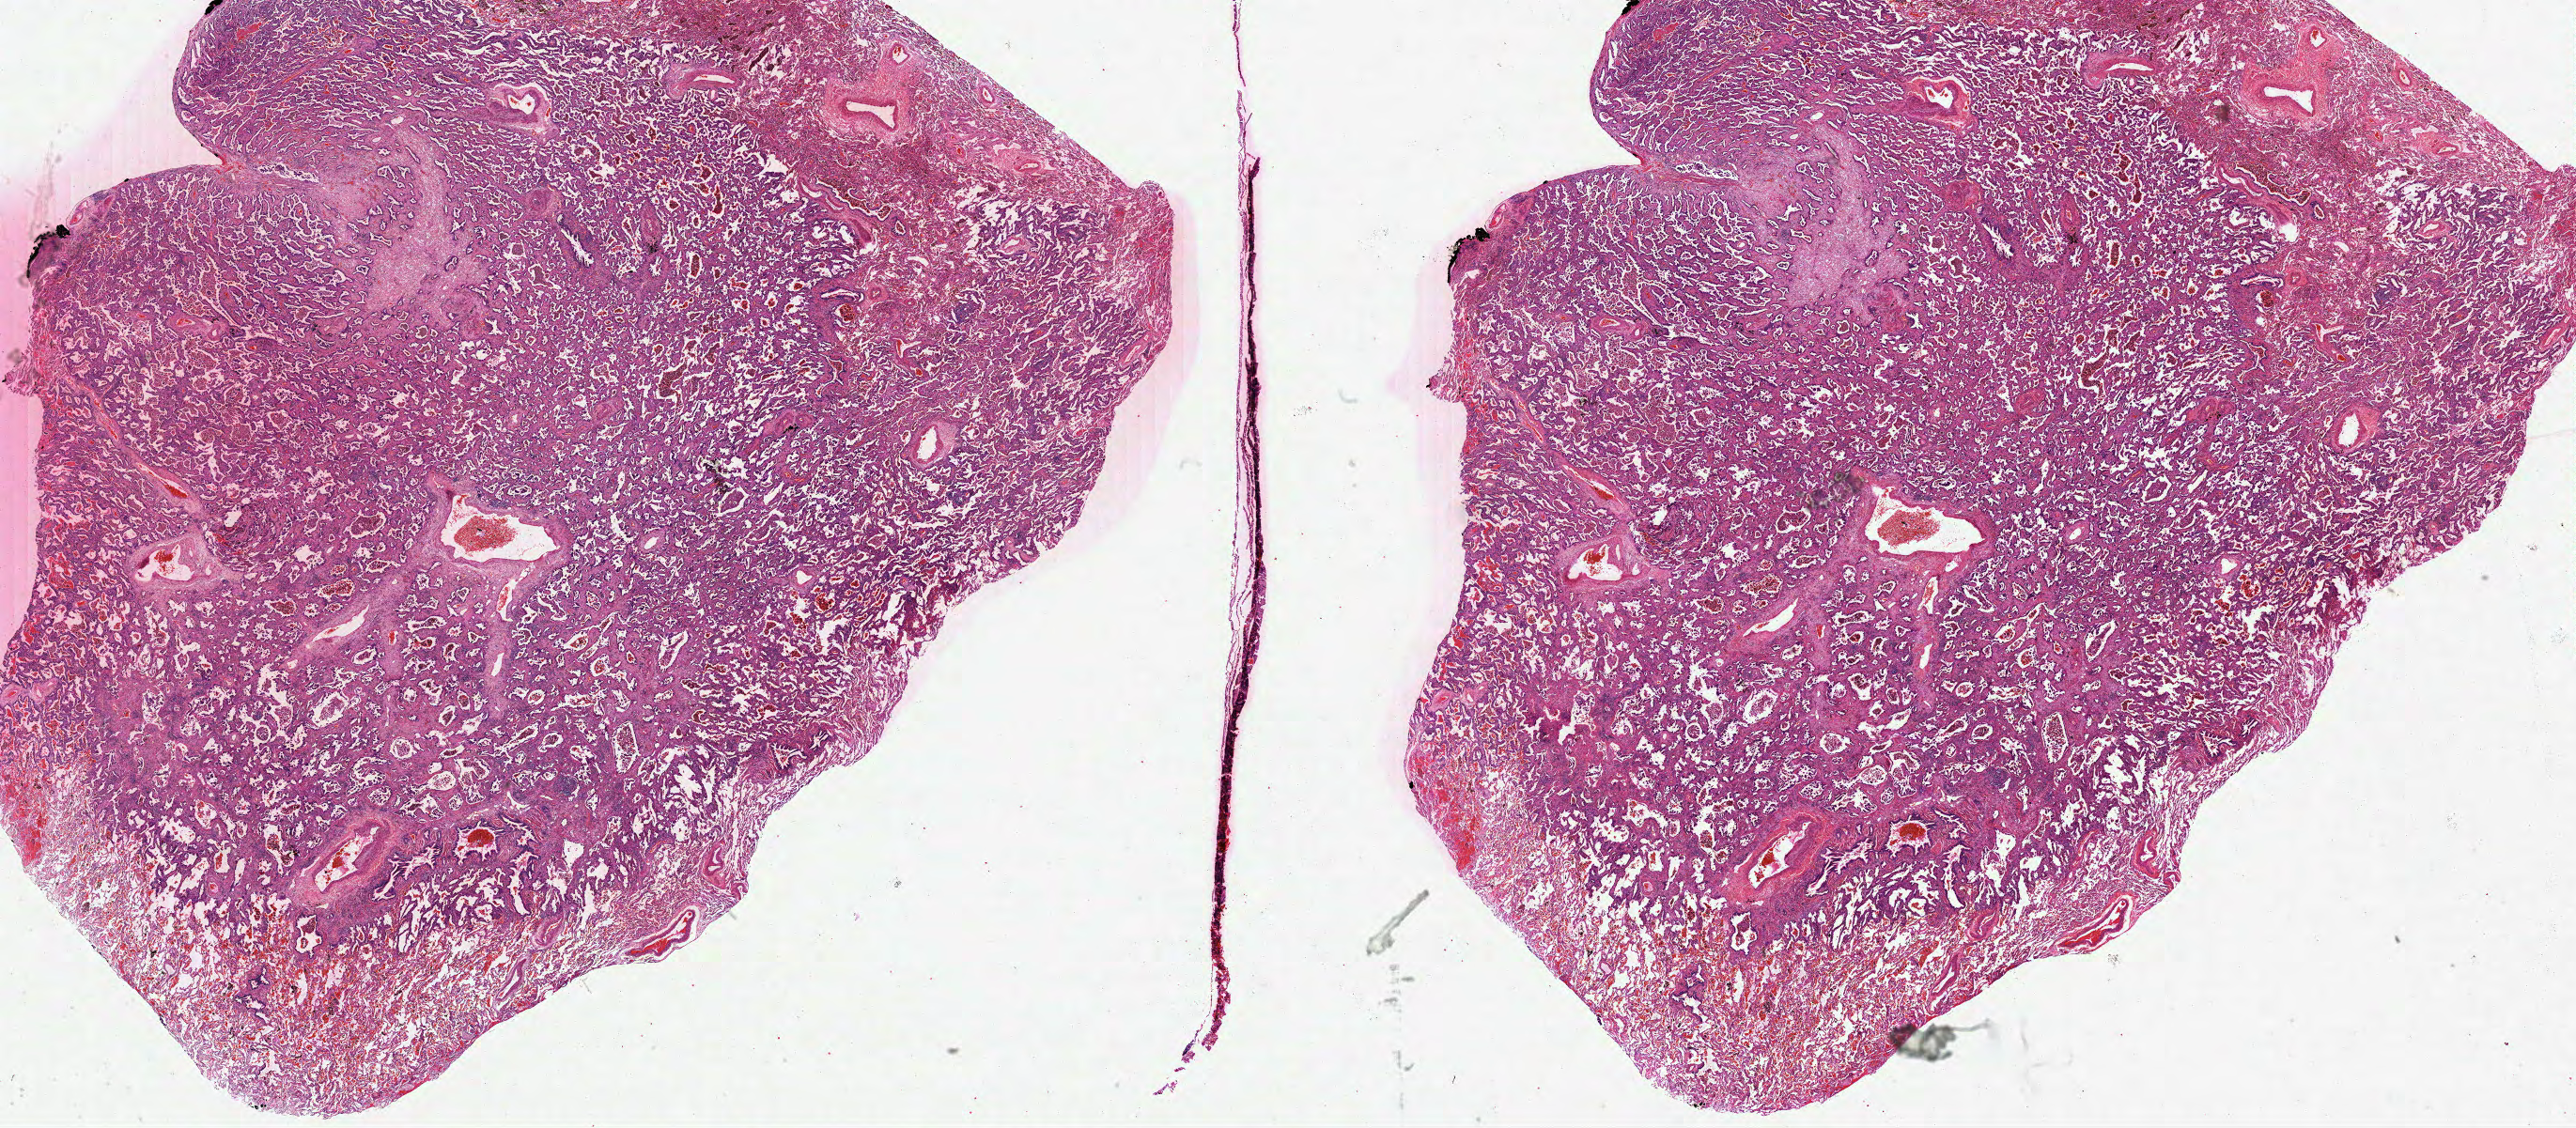
Whole-slide histology image, Hematoxylin and eosin (H&E) stained — a low-resolution overview of the entire scanned area, about 44.2 x 19.4 mm, formalin-fixed paraffin-embedded (FFPE) diagnostic section, sample: primary tumour, lung. Female patient; age at initial diagnosis 67 years.
Histologic diagnosis: Adenocarcinoma, NOS. AJCC pathologic stage: IB.